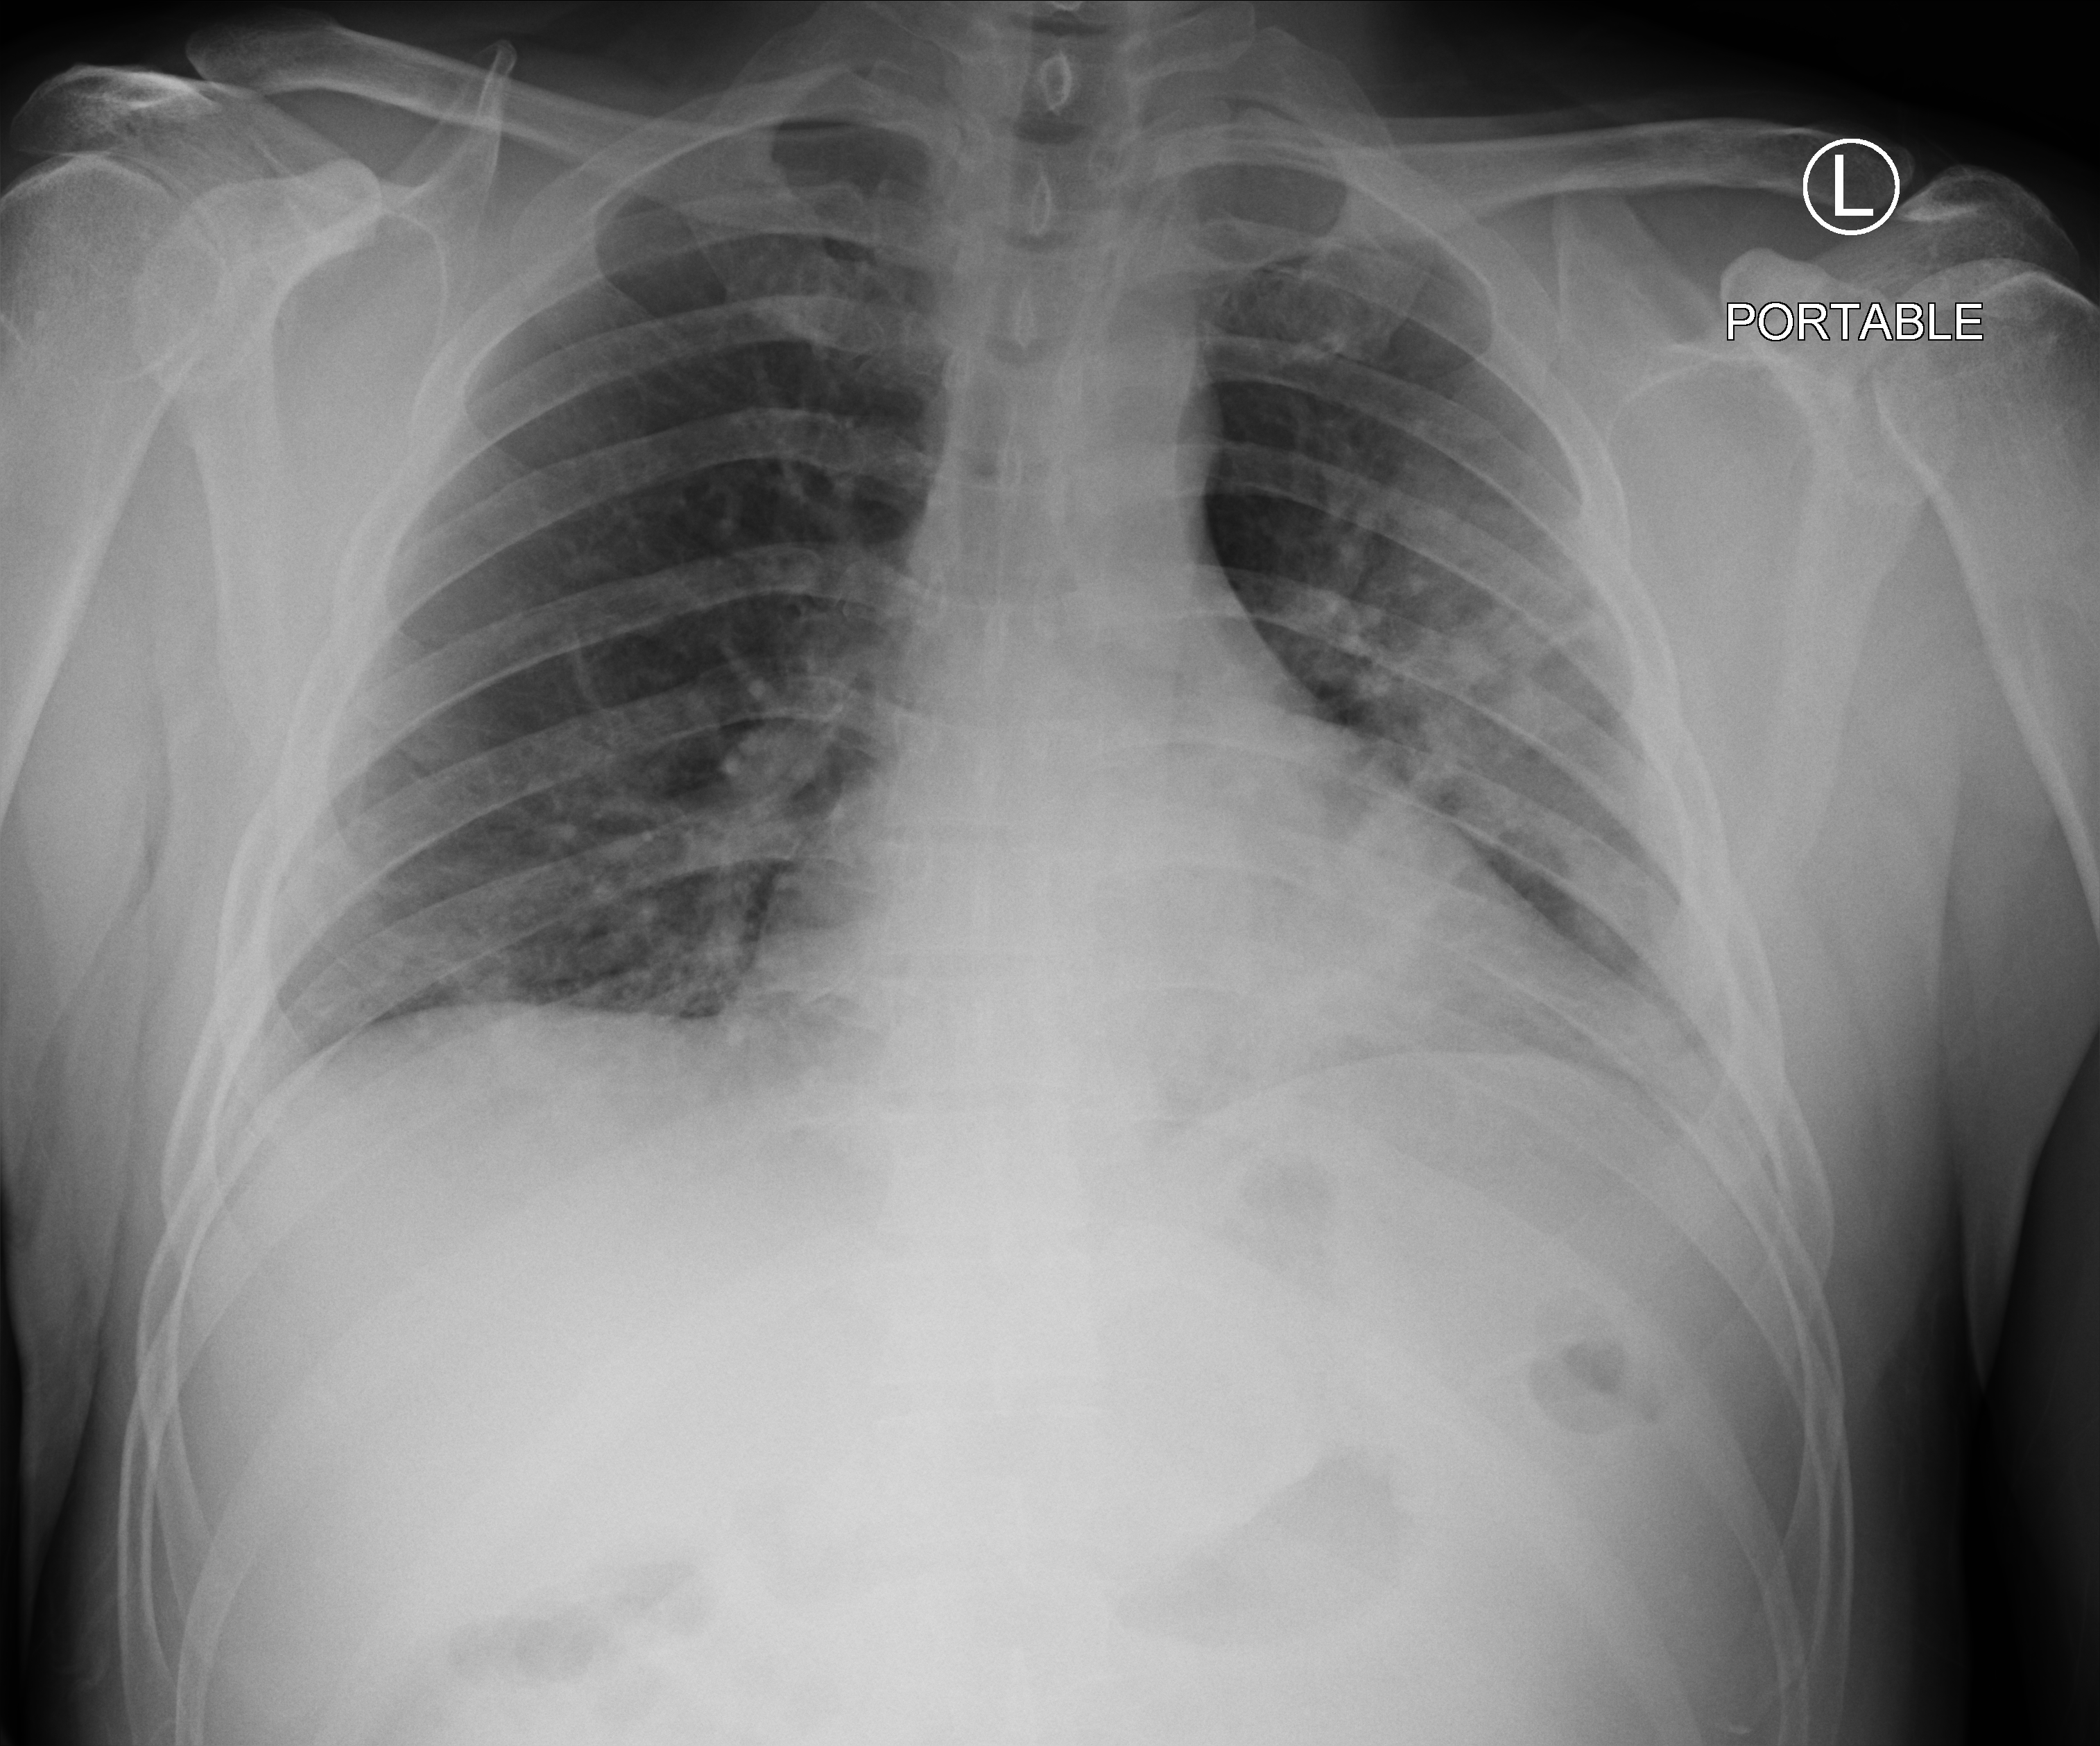
Chest X-ray (portable). Patient hospitalised with COVID-19; male, aged 18–59 years.
From the hospital-stay record, not from the radiograph (when in the stay this image was taken is not recorded): admitted to intensive care during this hospital stay: no.